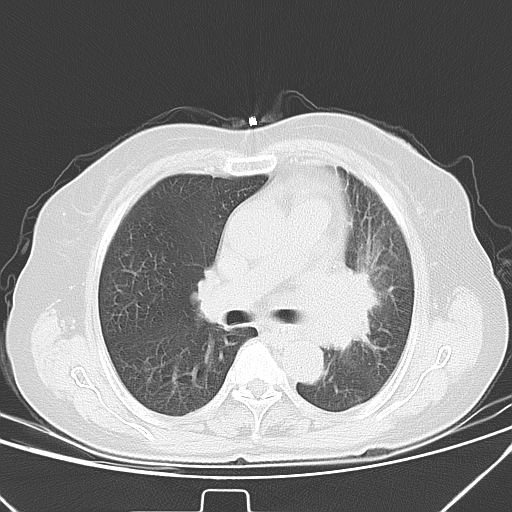
Chest CT, one axial slice; position 24 of 40 along the scan axis; 120 kVp; lung window (W 1500 / L -600 HU); 5 mm slice thickness; 512 × 512 image matrix, field of view 331 × 331 mm. Female patient, age 59 years. Case-level facts recorded for this patient, not image findings: clinical TNM (as recorded): T3 N1 M0.
Structures marked on this image (rectangle marked by the reading radiologist):
- lung tumour (recorded histology: small cell carcinoma): box from (x=327, y=255) to (x=387, y=356) px